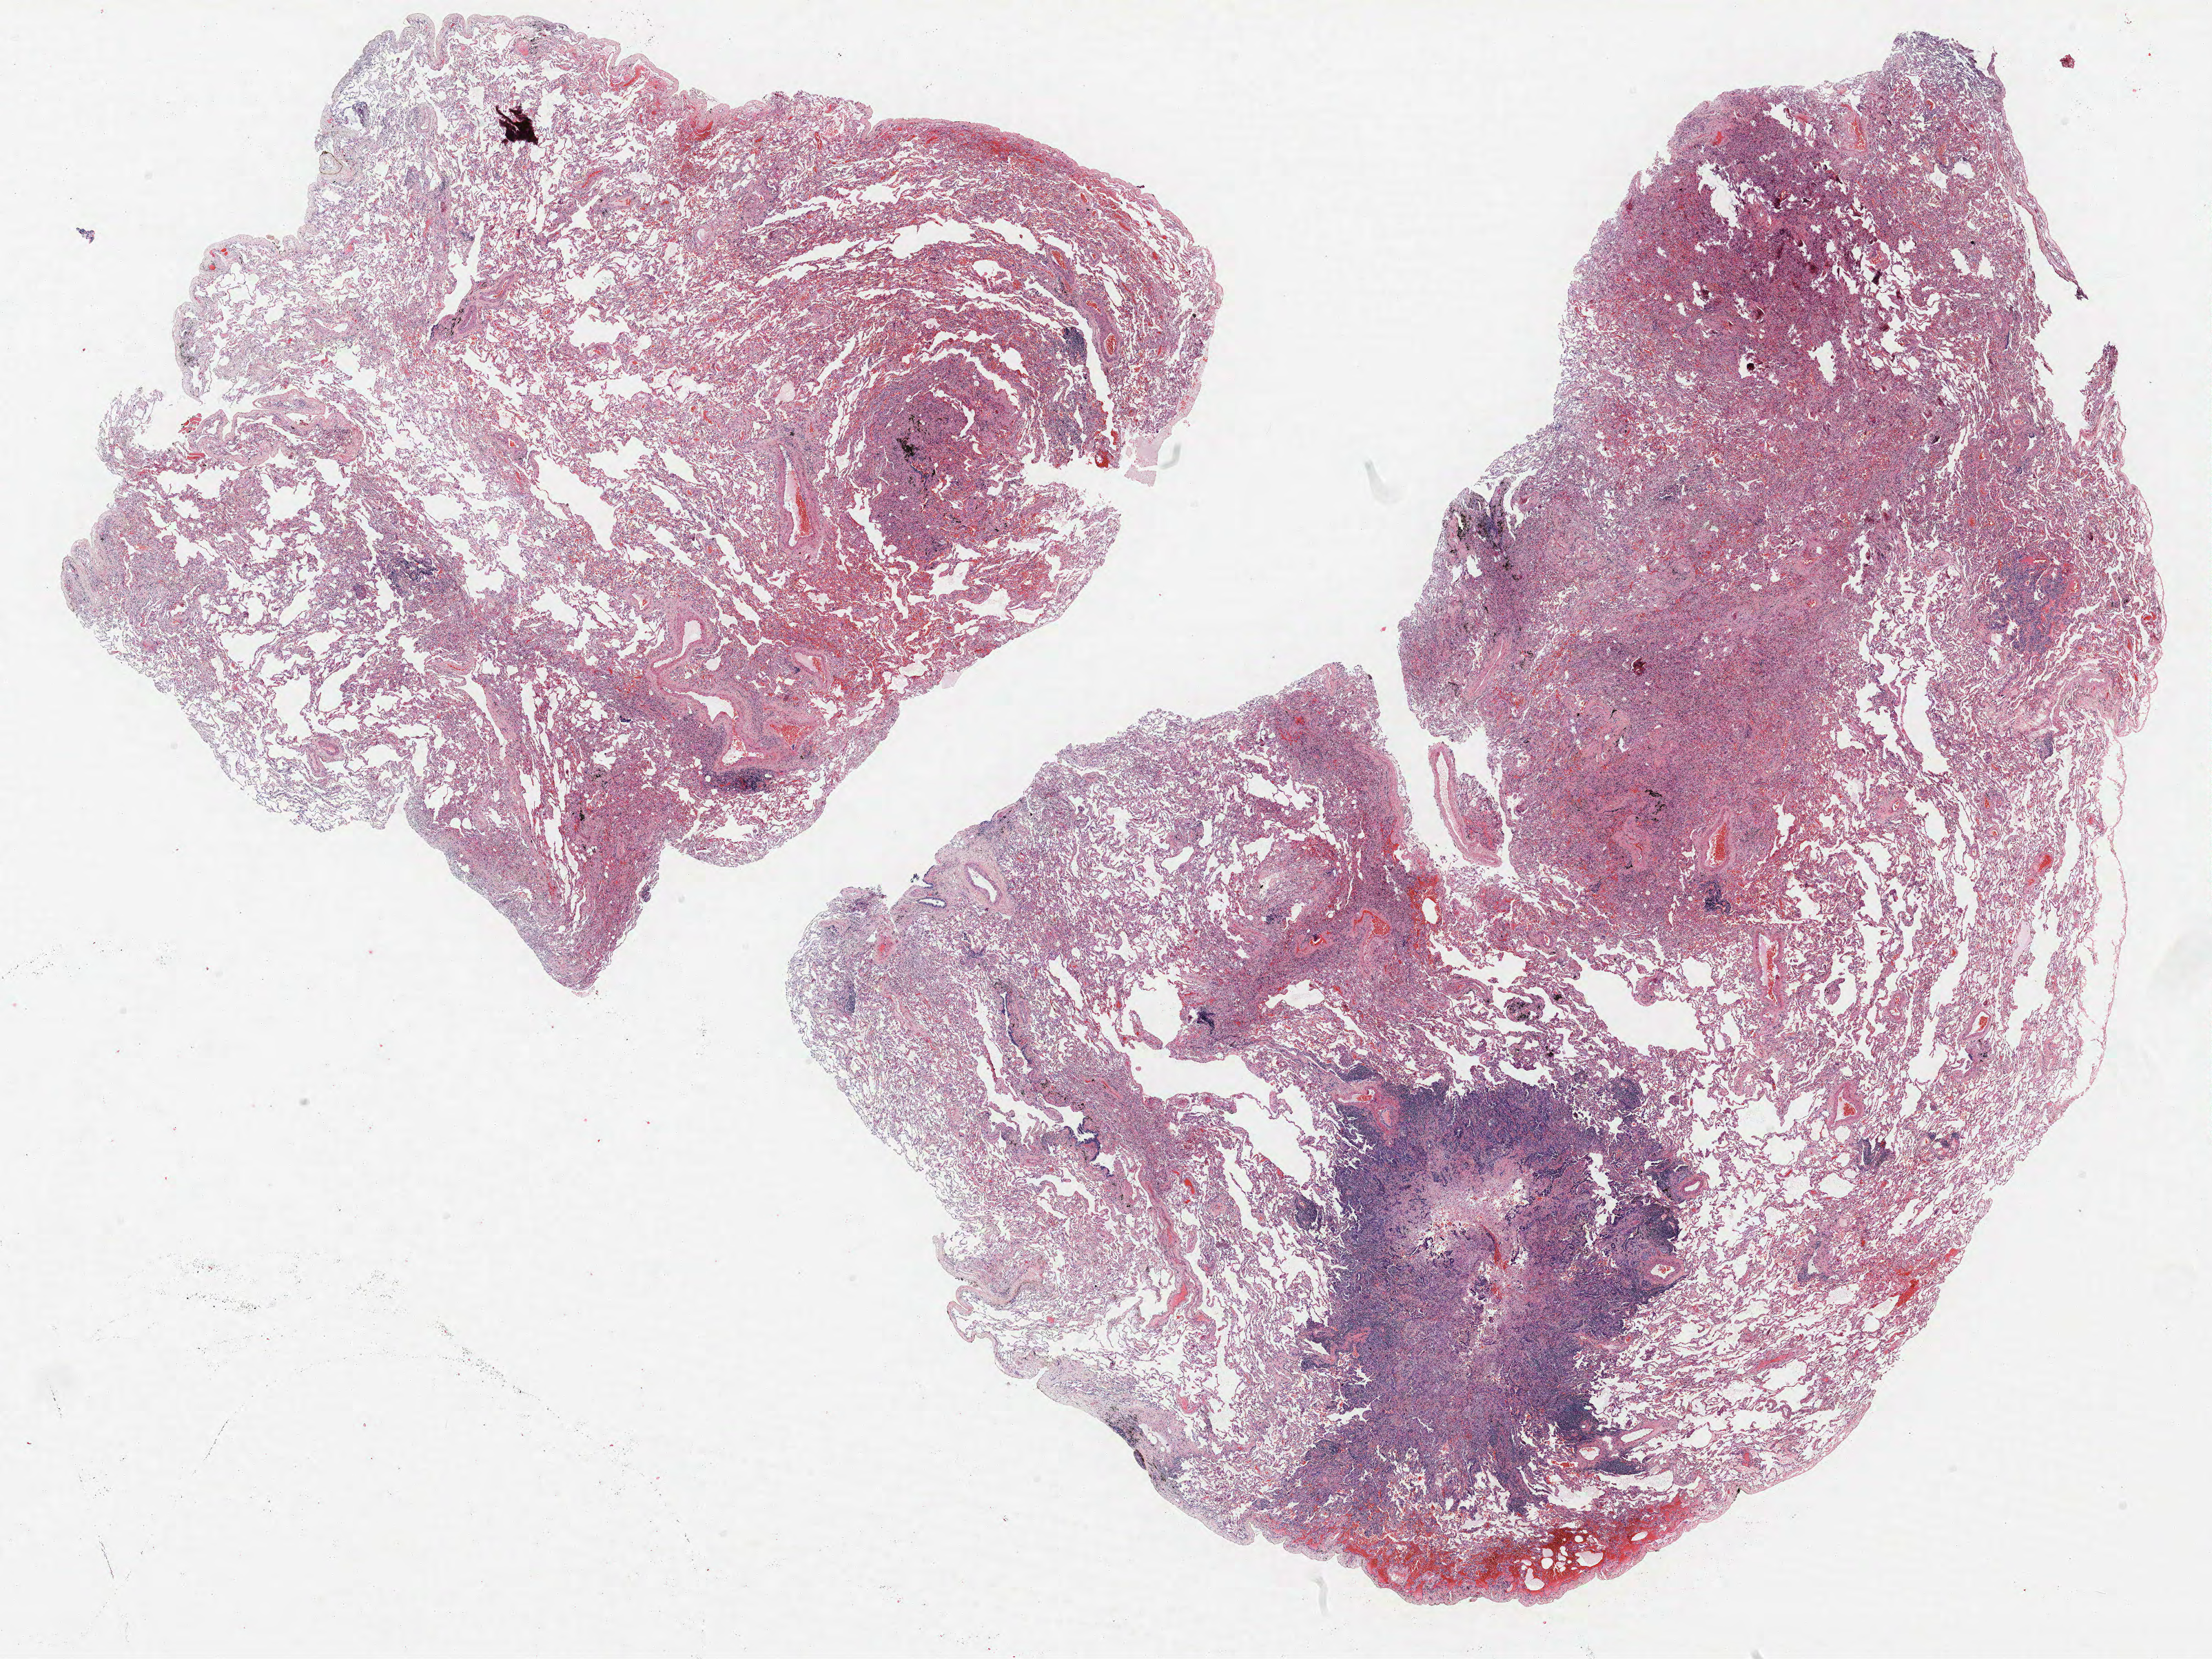
H&E whole-slide image, whole scanned area (about 25.7 x 19.3 mm, from a 40x scan) shown as a low-resolution overview; formalin-fixed paraffin-embedded (FFPE) section; lung. Female patient, aged 65 at enrolment.
Participant's lung-cancer diagnosis: Adenocarcinoma, NOS.